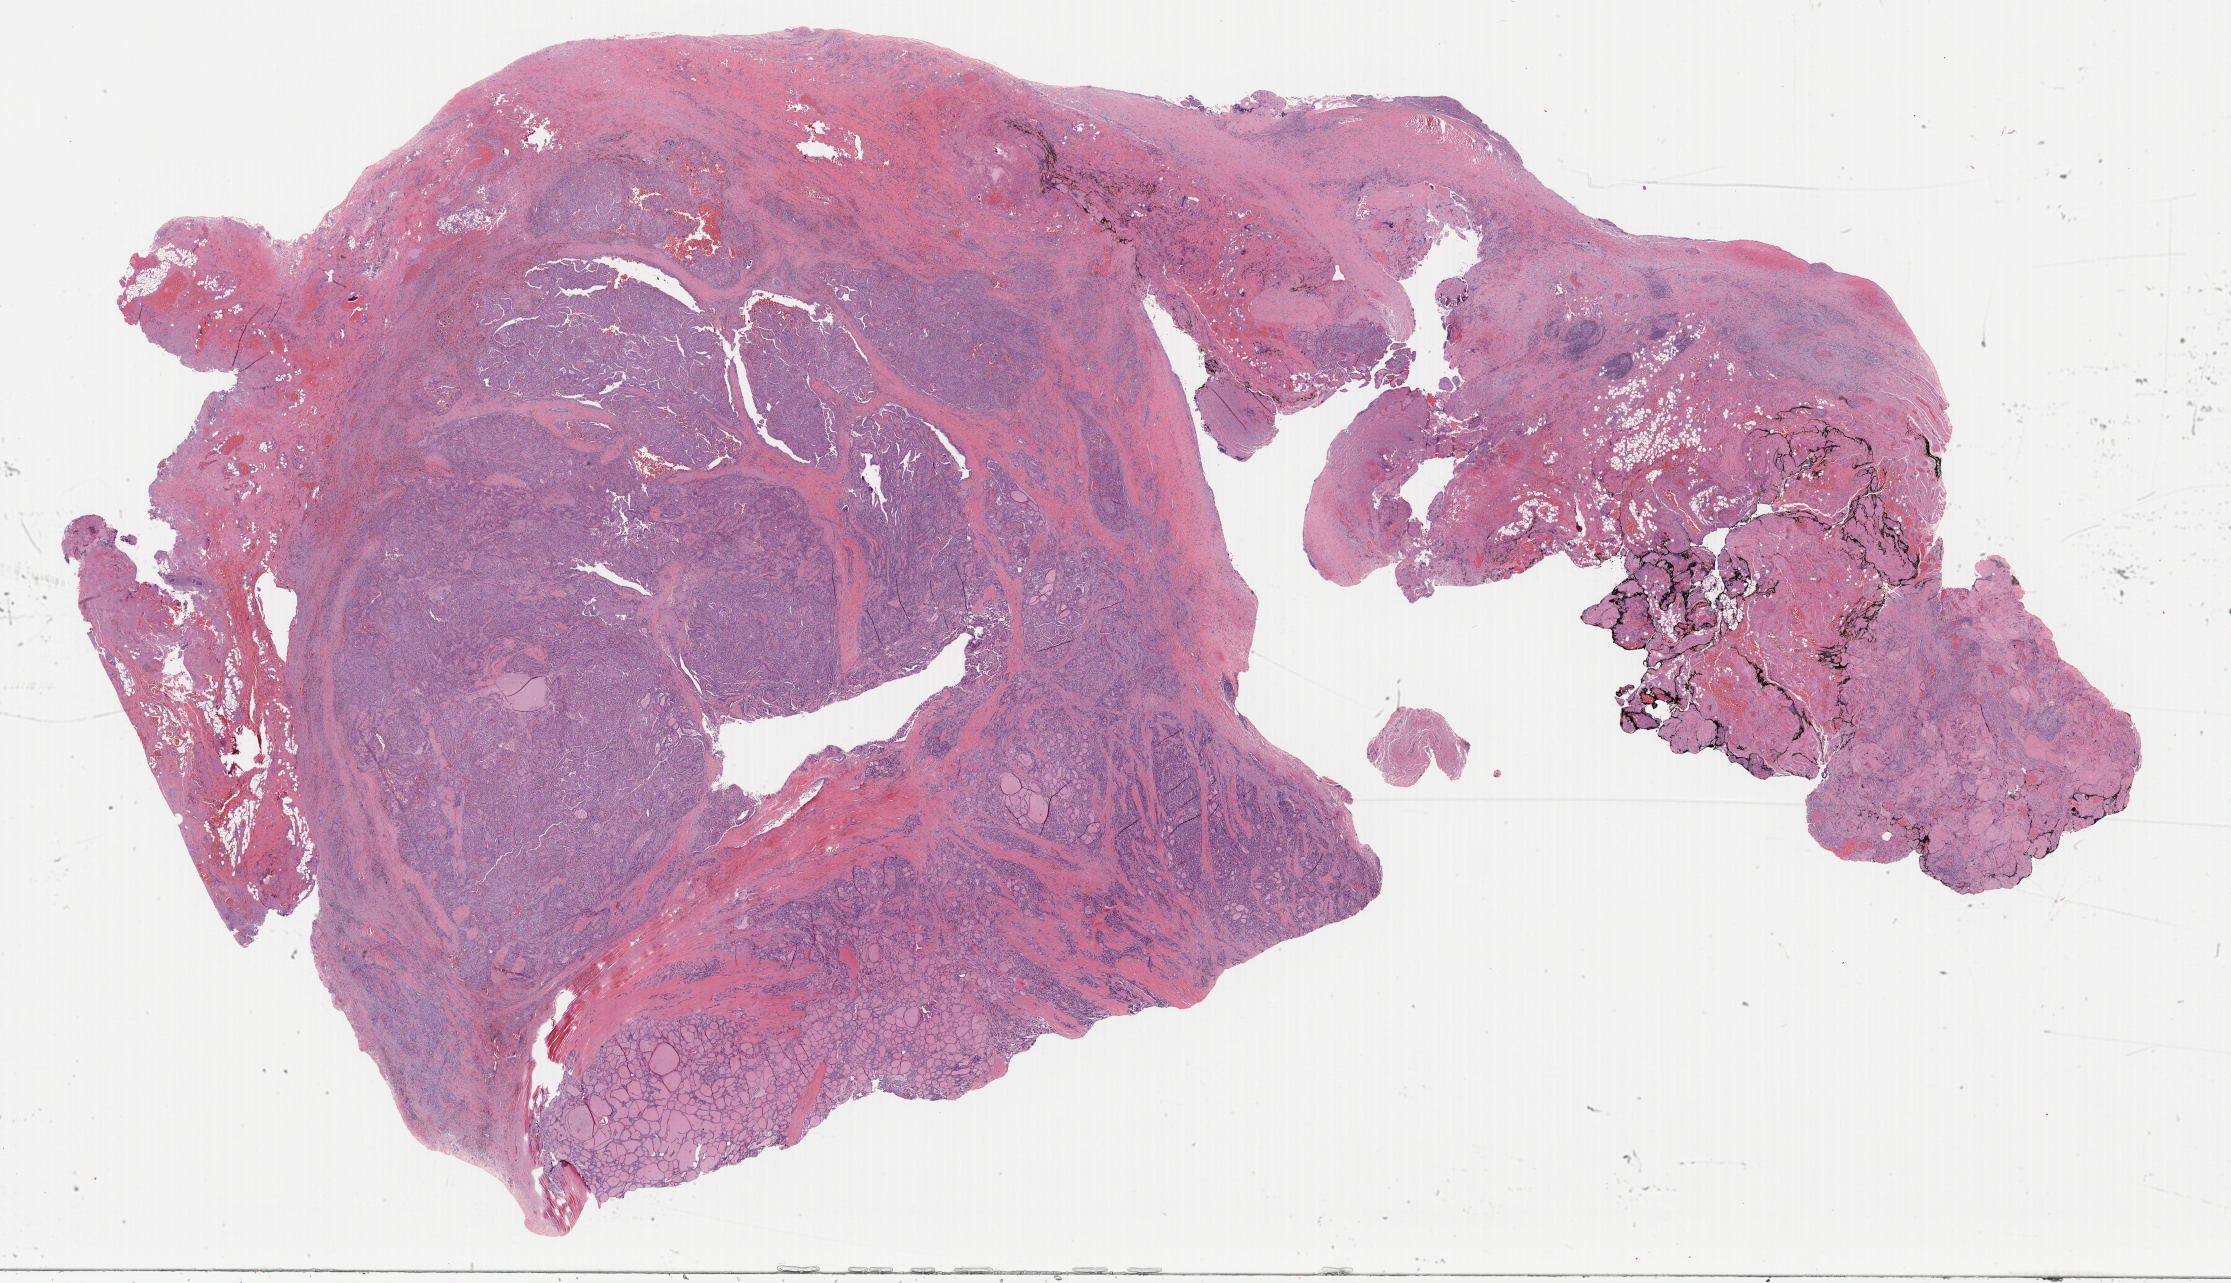
Whole-slide histology image, H&E-stained, a low-resolution overview of the entire scanned area, about 35.2 x 20.3 mm (from a 40x scan); formalin-fixed paraffin-embedded (FFPE) diagnostic section; sample: primary tumour, thyroid. Male, age 40 years at initial diagnosis.
Histologic diagnosis: Papillary adenocarcinoma, NOS (thyroid gland).